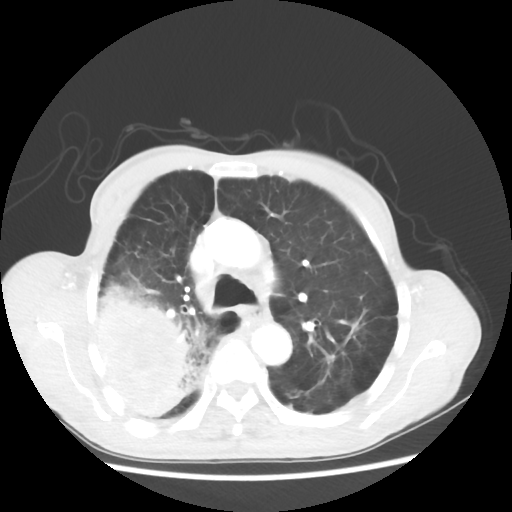
Chest CT, one axial slice. Slice 37 of 58 in the series (ordered by position). Reconstruction kernel STANDARD. 100 kVp. Lung window (W 1500 / L -600 HU). 5 mm slice thickness. 512 × 512 image matrix, field of view 351 × 351 mm. Male patient, age 75 years. Case-level facts recorded for this patient, not image findings: clinical TNM (as recorded): T4 N1 M1.
Annotated regions visible in this slice (bounding box drawn by a radiologist):
- lung tumour (recorded histology: adenocarcinoma): box from (x=98, y=273) to (x=215, y=424) px